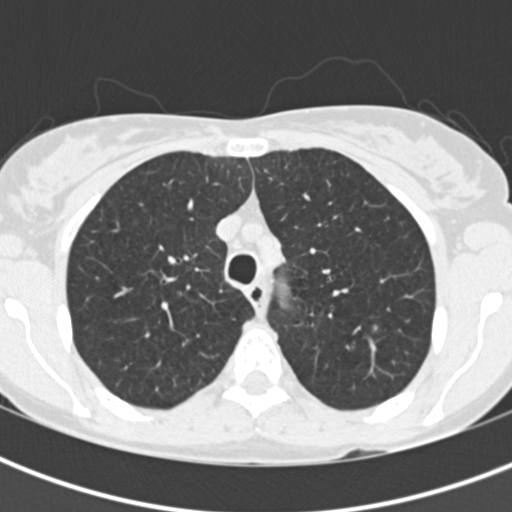
Axial slice from a low-dose chest CT screening exam, first (baseline) screen, lung window (W 1500 / L -600 HU), 2 mm slice thickness, standard (soft-tissue) reconstruction kernel (B30f), slice 49 of 199 in the series. Female, age 56 years at enrolment. Current smoker at enrolment.
Expert reader's lesion annotation, bounding box <361,305,401,347> (left, top, right, bottom; pixels). The exam's reader record, not a measurement of the box and not confirmed to be the same lesion: non-calcified nodule or mass ≥4 mm, right upper lobe, 6 × 5 mm, poorly defined margins, ground glass attenuation. Note: the box lies in the patient's left hemithorax on this image, whereas the reader's record names the right lung; they may be different findings. Official screen result: positive, change unspecified: nodule(s) >= 4 mm or enlarging nodule(s), mass(es), or other non-specific abnormalities suspicious for lung cancer. Participant outcome: lung cancer diagnosed 124 days after this screen — small cell carcinoma, NOS, left lower lobe, stage IV (AJCC 6th edition), 80 mm at pathology.